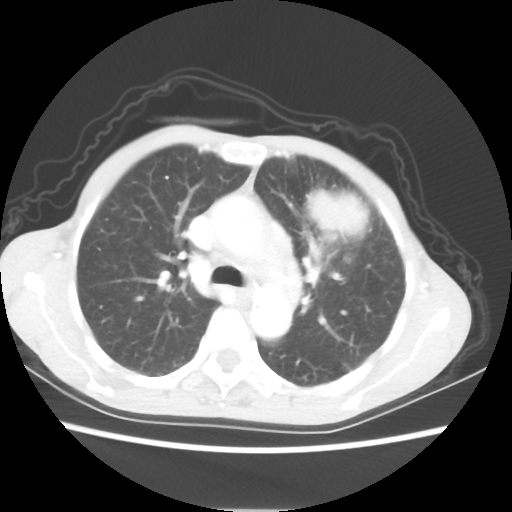
Chest CT, one axial slice. 80 kVp. Lung window (W 1500 / L -600 HU). 5 mm slice thickness. 512 × 512 image matrix, field of view 331 × 331 mm. Female patient, age 60 years. Case-level facts recorded for this patient, not image findings: clinical TNM (as recorded): T4 N1 M0.
Structures marked on this image (bounding box drawn by a radiologist):
- lung tumour (recorded histology: adenocarcinoma): bounding box (x1, y1, x2, y2) in pixels: (302, 185, 374, 248)